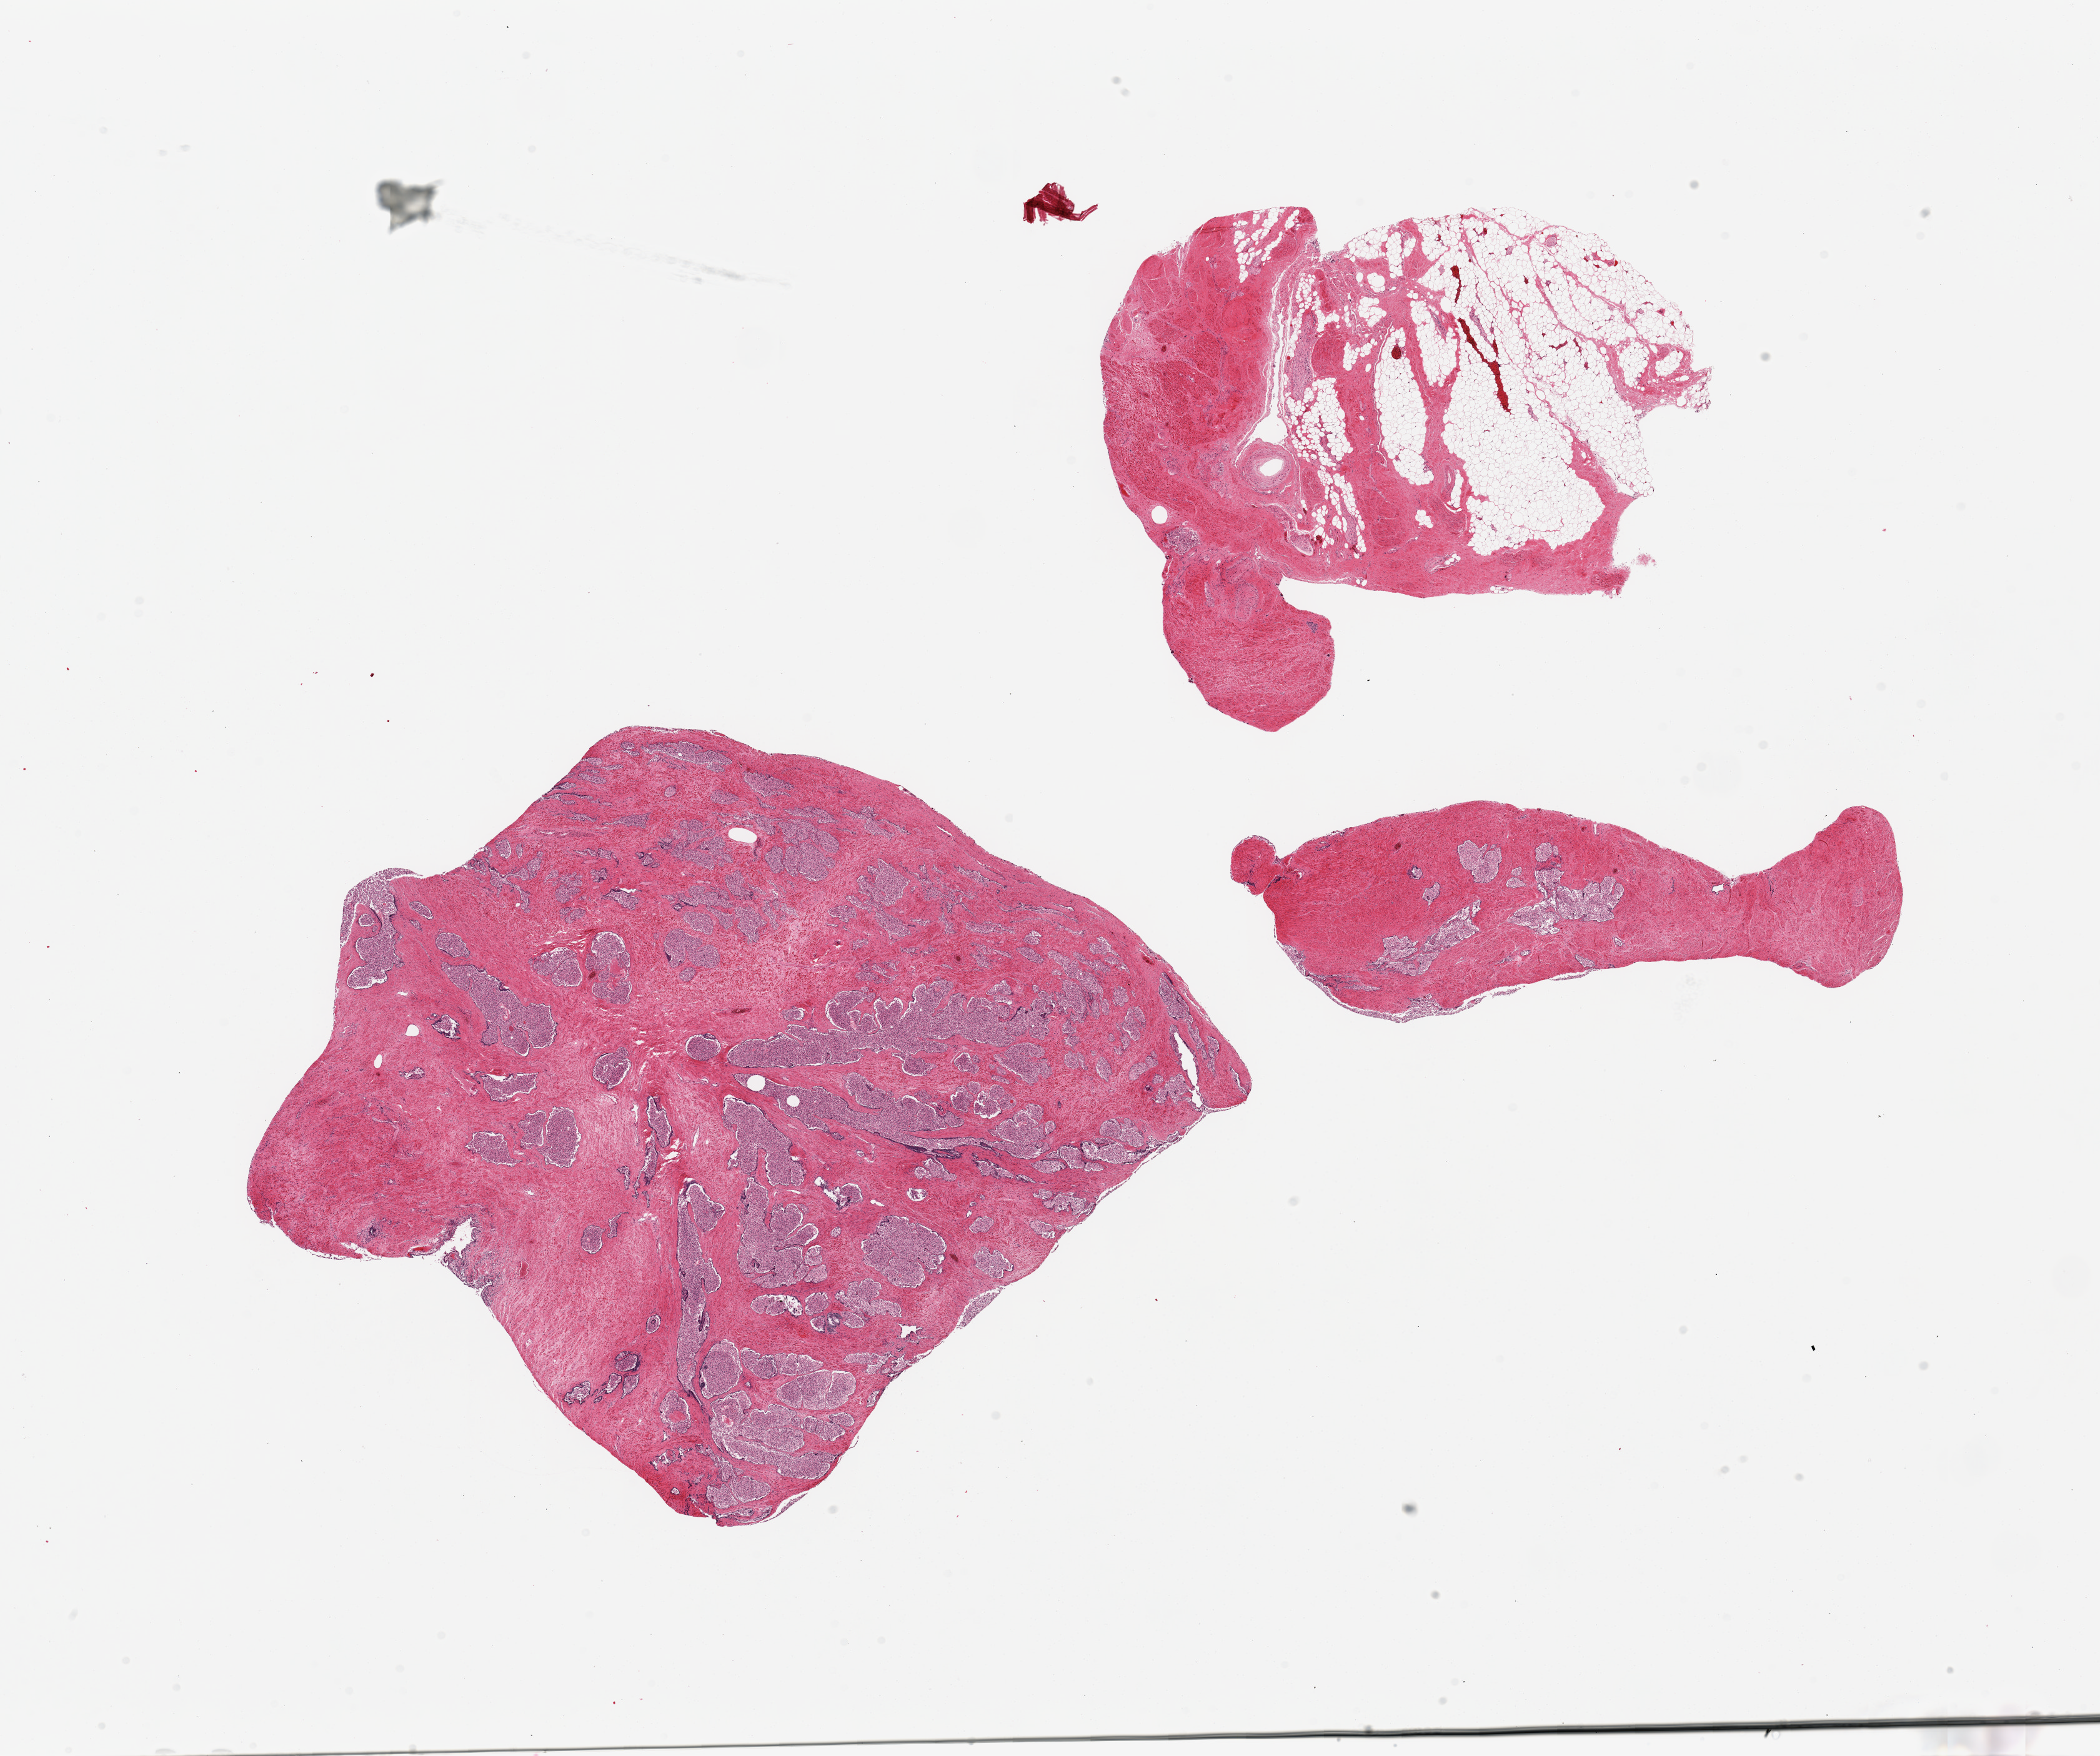
Whole-slide image, H&E stain, shown as a low-resolution overview of the whole scanned area (about 26.6 x 22.2 mm, from a 20x scan); PAXgene-fixed paraffin-embedded (PFPE) section; sampled site (target tissue): prostate; tissue donor sample. Donor: male.
Review note (as recorded): 3 pieces; glands totally autolyzed, stroma preserved; 1 piece appears to be periprostatic fibrofatty tissue.